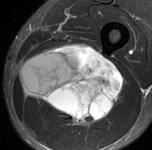
MRI of an extremity soft-tissue mass, one axial slice. Position 55 of 90 along the scan axis. STIR. MR volume resampled by the dataset authors to the PET/CT grid (not the native acquisition matrix). 152 × 150 image matrix. Male patient. Case-level facts recorded for this patient, not image findings: histological type: undifferentiated pleomorphic liposarcoma; grade: high; site of the primary tumour: left thigh.
Annotated regions visible in this slice (expert contour drawn on MRI and transferred to this co-registered scan by the dataset authors):
- gross tumour volume including surrounding oedema: bounding box (x1, y1, x2, y2) in pixels: (20, 43, 124, 127)
- gross tumour volume (mass): (20, 43, 124, 125)